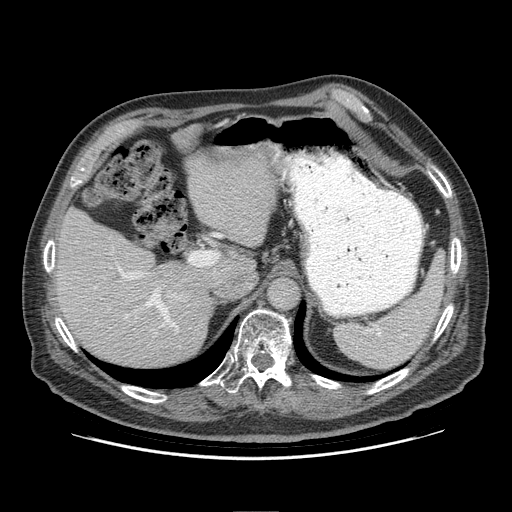
Contrast-enhanced abdominal CT (liver protocol), one axial slice; position 63 of 95 along the scan axis; reconstruction kernel STANDARD; 140 kVp; soft-tissue window (W 400 / L 40 HU); 2.5 mm slice thickness; 512 × 512 image matrix. Case-level facts recorded for this patient, not image findings: diagnosis: hepatocellular carcinoma (patient treated with transarterial chemoembolisation; whether this scan precedes or follows treatment is not stated here); TNM stage (as recorded): Stage-IVB; Child-Pugh class: A; tumour differentiation: well differentiated; tumour nodularity: uninodular.
Outlined on this slice (semi-automatically segmented with operator editing):
- abdominal aorta: bounding box (x1, y1, x2, y2) in pixels: (268, 277, 299, 310)
- liver parenchyma outside the tumour (the mass and vessels are separate outlines, so this box may not span the whole liver): (54, 124, 276, 366)
- liver vessels: (118, 267, 178, 328)